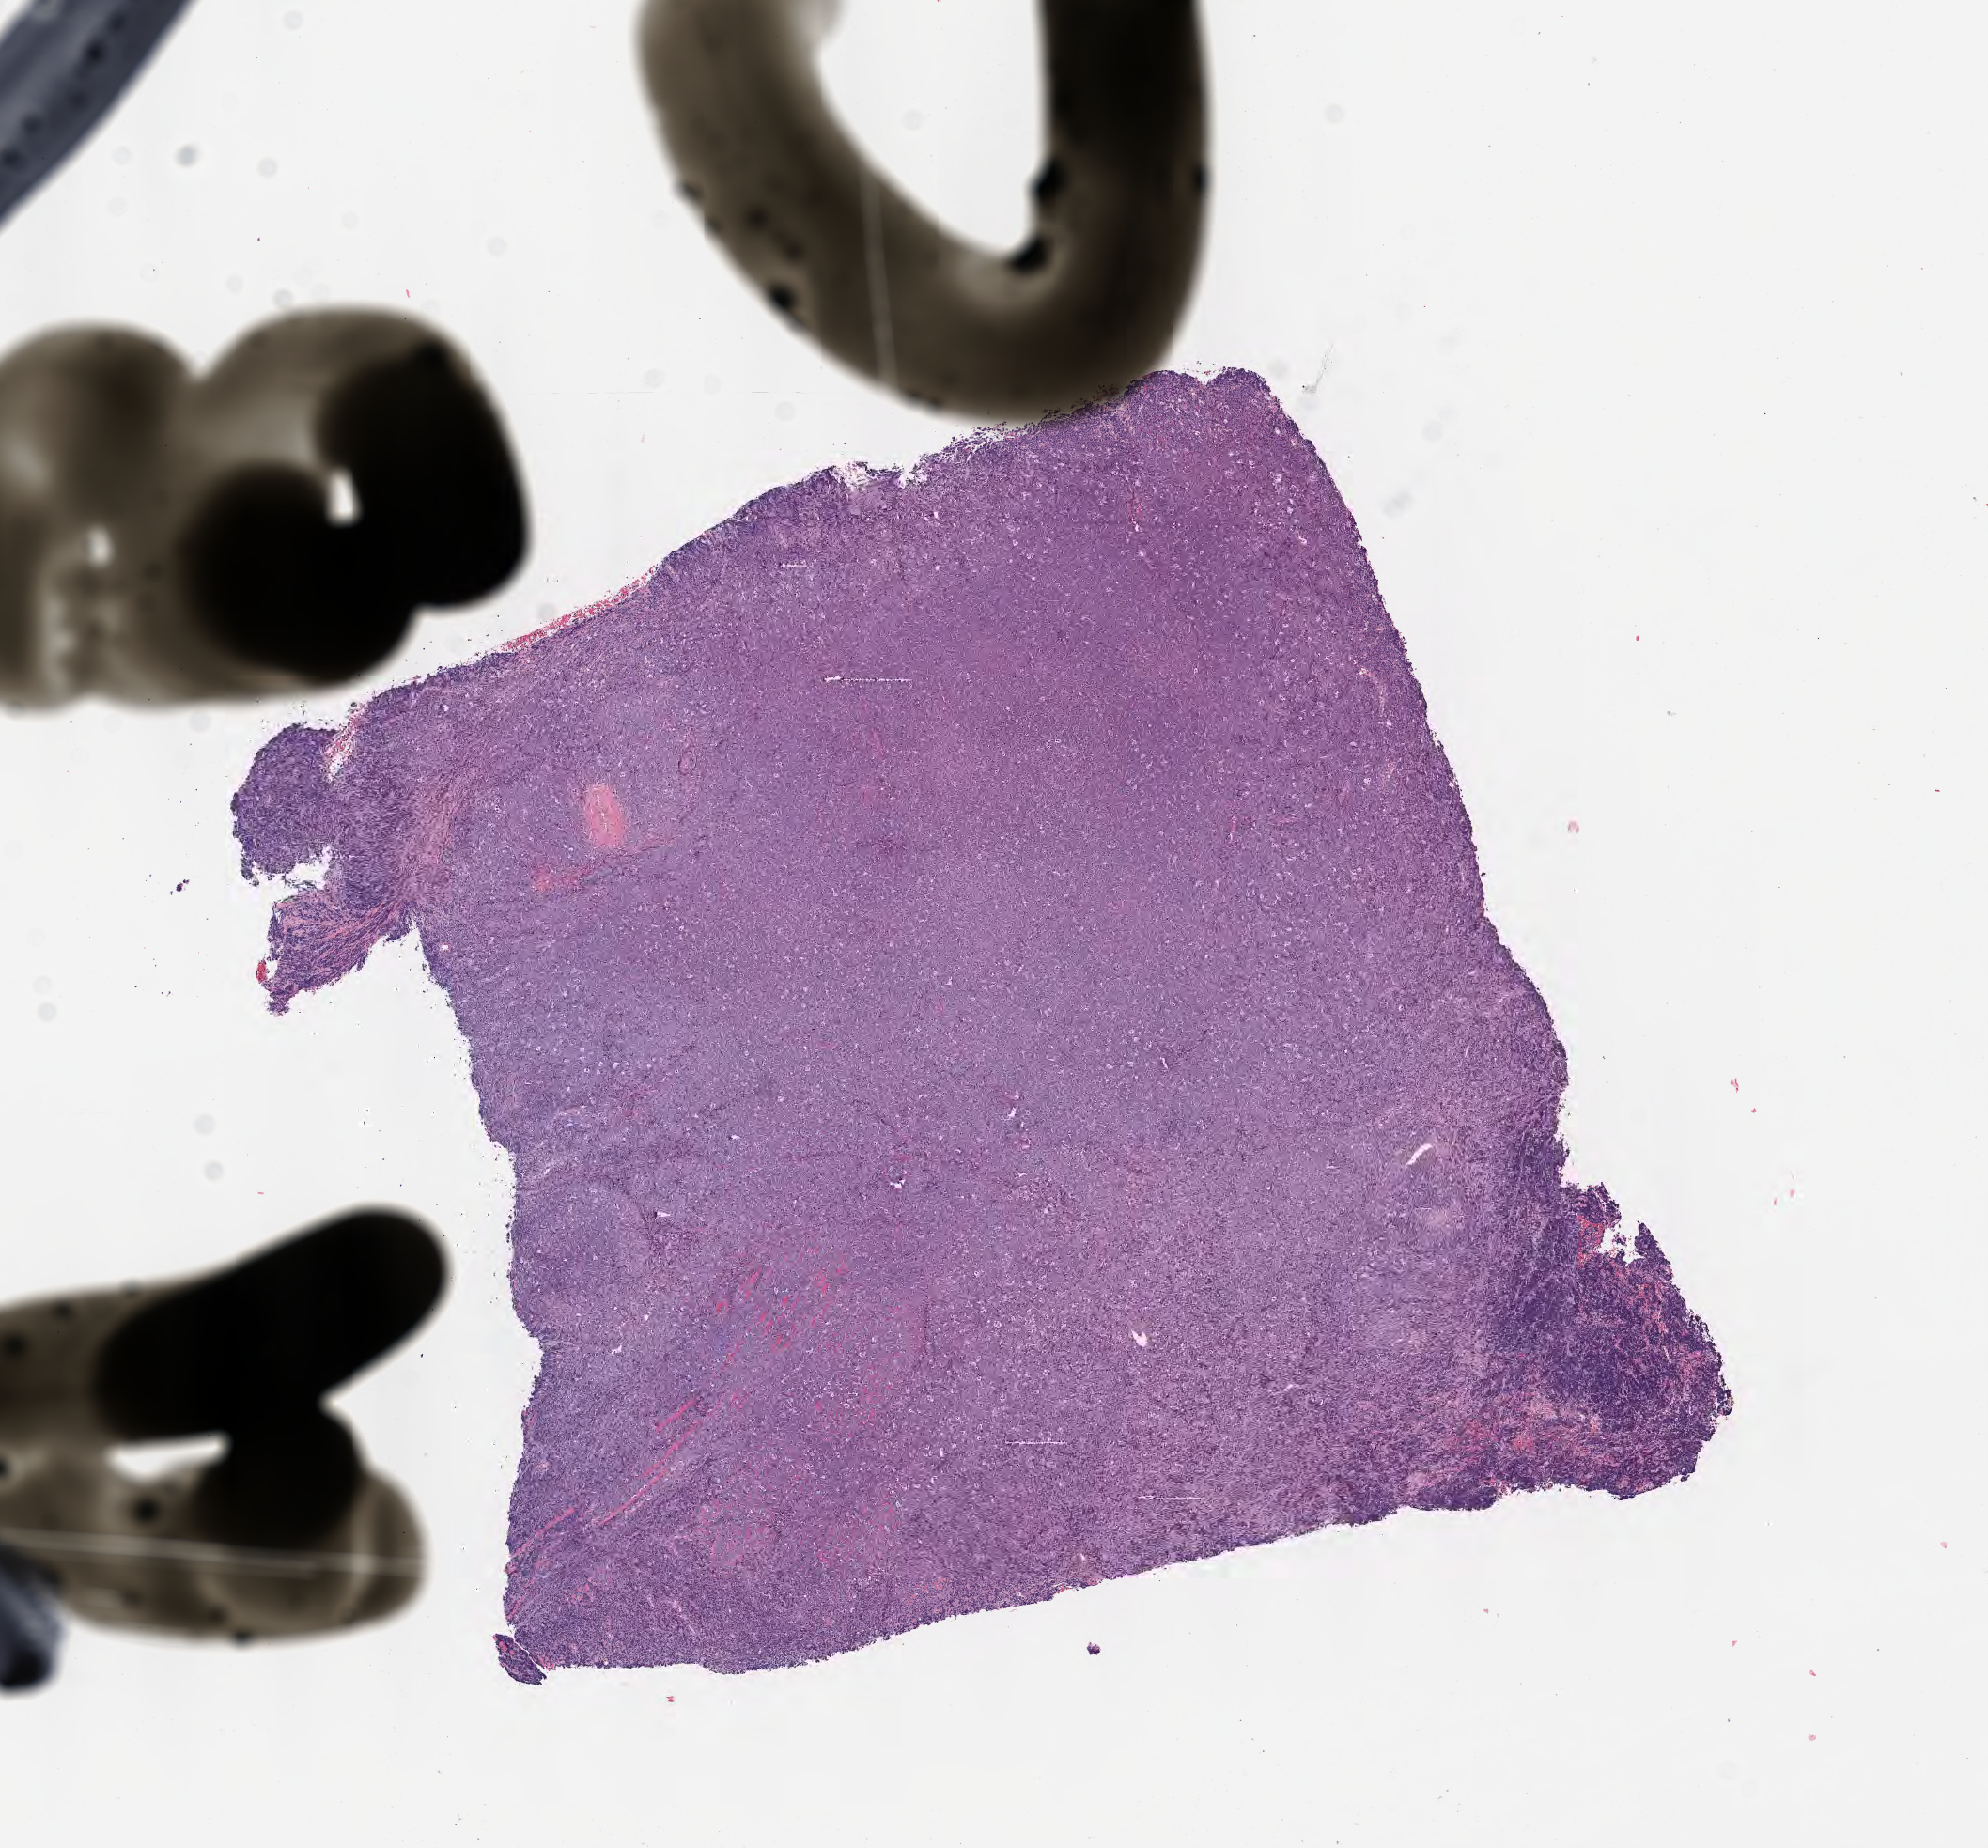
Whole-slide image, haematoxylin and eosin stain, whole scanned area (about 8.6 x 7.9 mm) shown as a low-resolution overview; formalin-fixed, paraffin-embedded (FFPE) tissue; specimen: primary tumor; site: cranium. Male patient; age at initial diagnosis 5 years.
Diagnosis: Burkitt lymphoma, NOS.